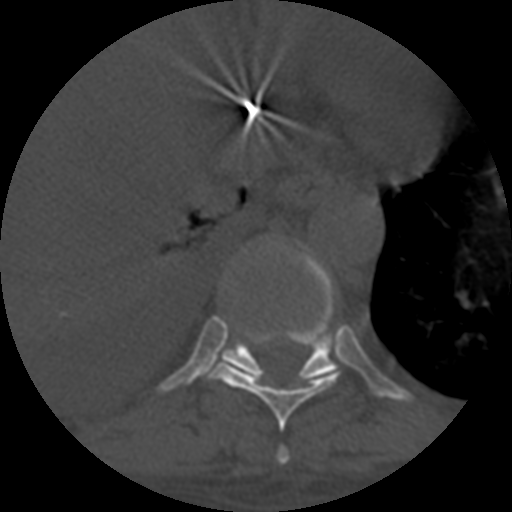
CT including the spine, one axial slice. Slice 369 of 708 in the series (ordered by position). 120 kVp. One of 3 acquisitions stored at this slice position. Bone window (W 1800 / L 400 HU). 512 × 512 image matrix, field of view 160 × 160 mm. Patient age 55 years. From the clinical record (not read from this slice): primary cancer: colon; vertebrae with lytic lesions (as recorded): T12, L1, L5.
Annotated regions visible in this slice (semi-automatic segmentation, software-assisted and operator-edited):
- T10 vertebra: bounding box <222,241,339,381> (left, top, right, bottom; pixels)
- T8 vertebra: <276,446,290,465>
- T9 vertebra: <207,324,341,431>